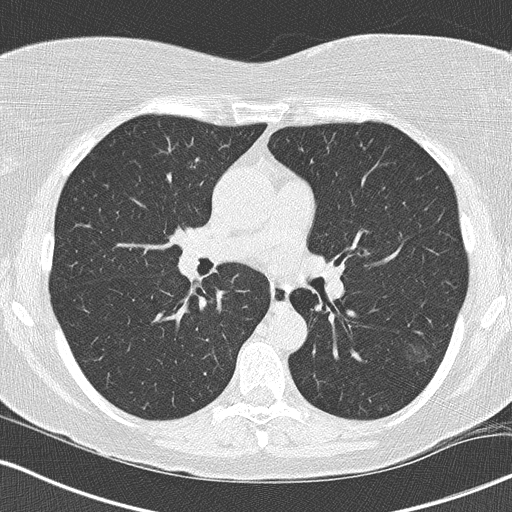
Axial slice from a low-dose chest CT screening exam. Third annual screen. Lung window (W 1500 / L -600 HU). Lung (sharp) reconstruction kernel (B50f). 120 kVp. 512 × 512 image matrix, field of view 327 × 327 mm. Female participant, aged 57 years at enrolment.
- Lesion marked by an expert reader, bounding box [x1, y1, x2, y2] px = [387, 327, 449, 376].
- The screening reader recorded 5 non-calcified nodules or masses ≥4 mm on this exam; which of them this box marks is not recorded.
- Official screen result: positive, other.